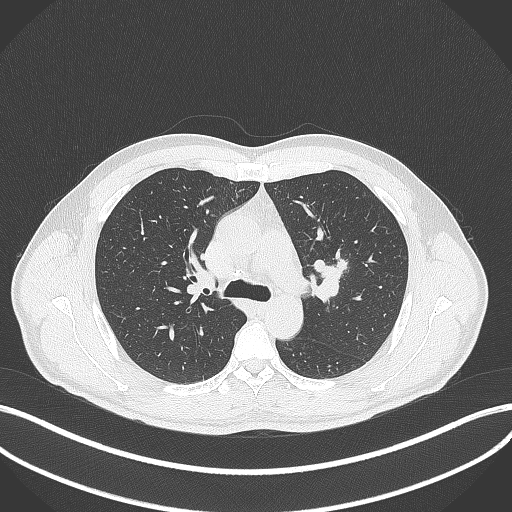
Chest CT, one axial slice; slice 279 of 392 in the series (ordered by position); 120 kVp; lung window (W 1500 / L -600 HU); 1 mm slice thickness; 512 × 512 image matrix. Male patient, age 50 years. Case-level facts recorded for this patient, not image findings: clinical TNM (as recorded): T1c N1 M1b.
Structures marked on this image (bounding box drawn by a radiologist):
- lung tumour (recorded histology: squamous cell carcinoma): box from (x=306, y=257) to (x=351, y=303) px